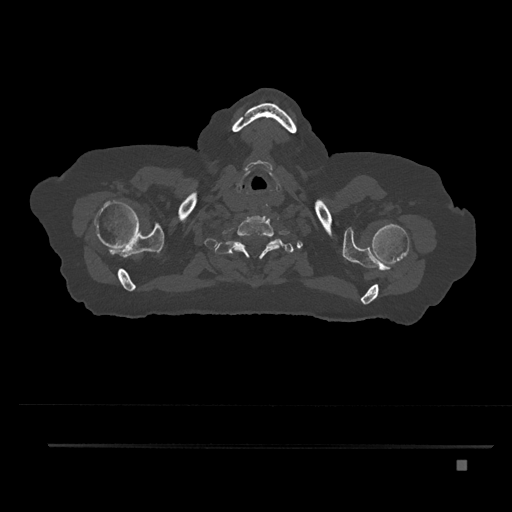
CT including the spine, one axial slice. Slice 715 of 797 in the series (ordered by position). Reconstruction kernel Br40s/3. 120 kVp. Bone window (W 1800 / L 400 HU). 0.5 mm slice thickness. 512 × 512 image matrix. Female patient, age 76 years. From the clinical record (not read from this slice): primary cancer: lung.
Outlined on this slice (semi-automatic segmentation, software-assisted and operator-edited):
- T1 vertebra: box from (x=223, y=239) to (x=280, y=257) px